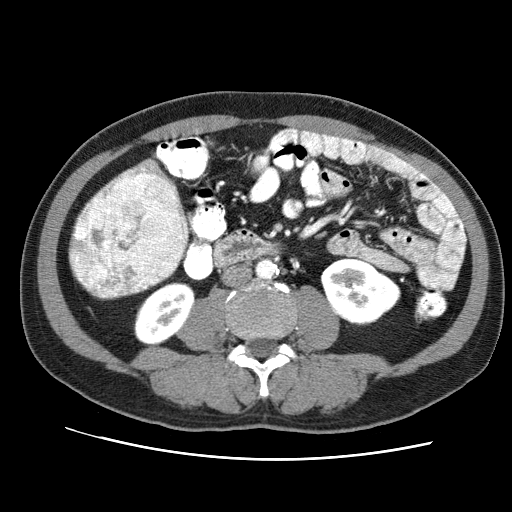
Contrast-enhanced abdominal CT (liver protocol), one axial slice. Slice 14 of 71 in the series (ordered by position). Reconstruction kernel STANDARD. 120 kVp. Soft-tissue window (W 400 / L 40 HU). 512 × 512 image matrix, field of view 360 × 360 mm. Case-level facts recorded for this patient, not image findings: diagnosis: hepatocellular carcinoma (patient treated with transarterial chemoembolisation; whether this scan precedes or follows treatment is not stated here); TNM stage (as recorded): Stage-II; Child-Pugh class: A; tumour differentiation: well differentiated.
Structures marked on this image (semi-automatic segmentation, software-assisted and operator-edited):
- liver parenchyma outside the tumour (the mass and vessels are separate outlines, so this box may not span the whole liver): bounding box <70,163,188,297> (left, top, right, bottom; pixels)
- mass: <68,168,188,299>
- liver vessels: <142,168,145,171>